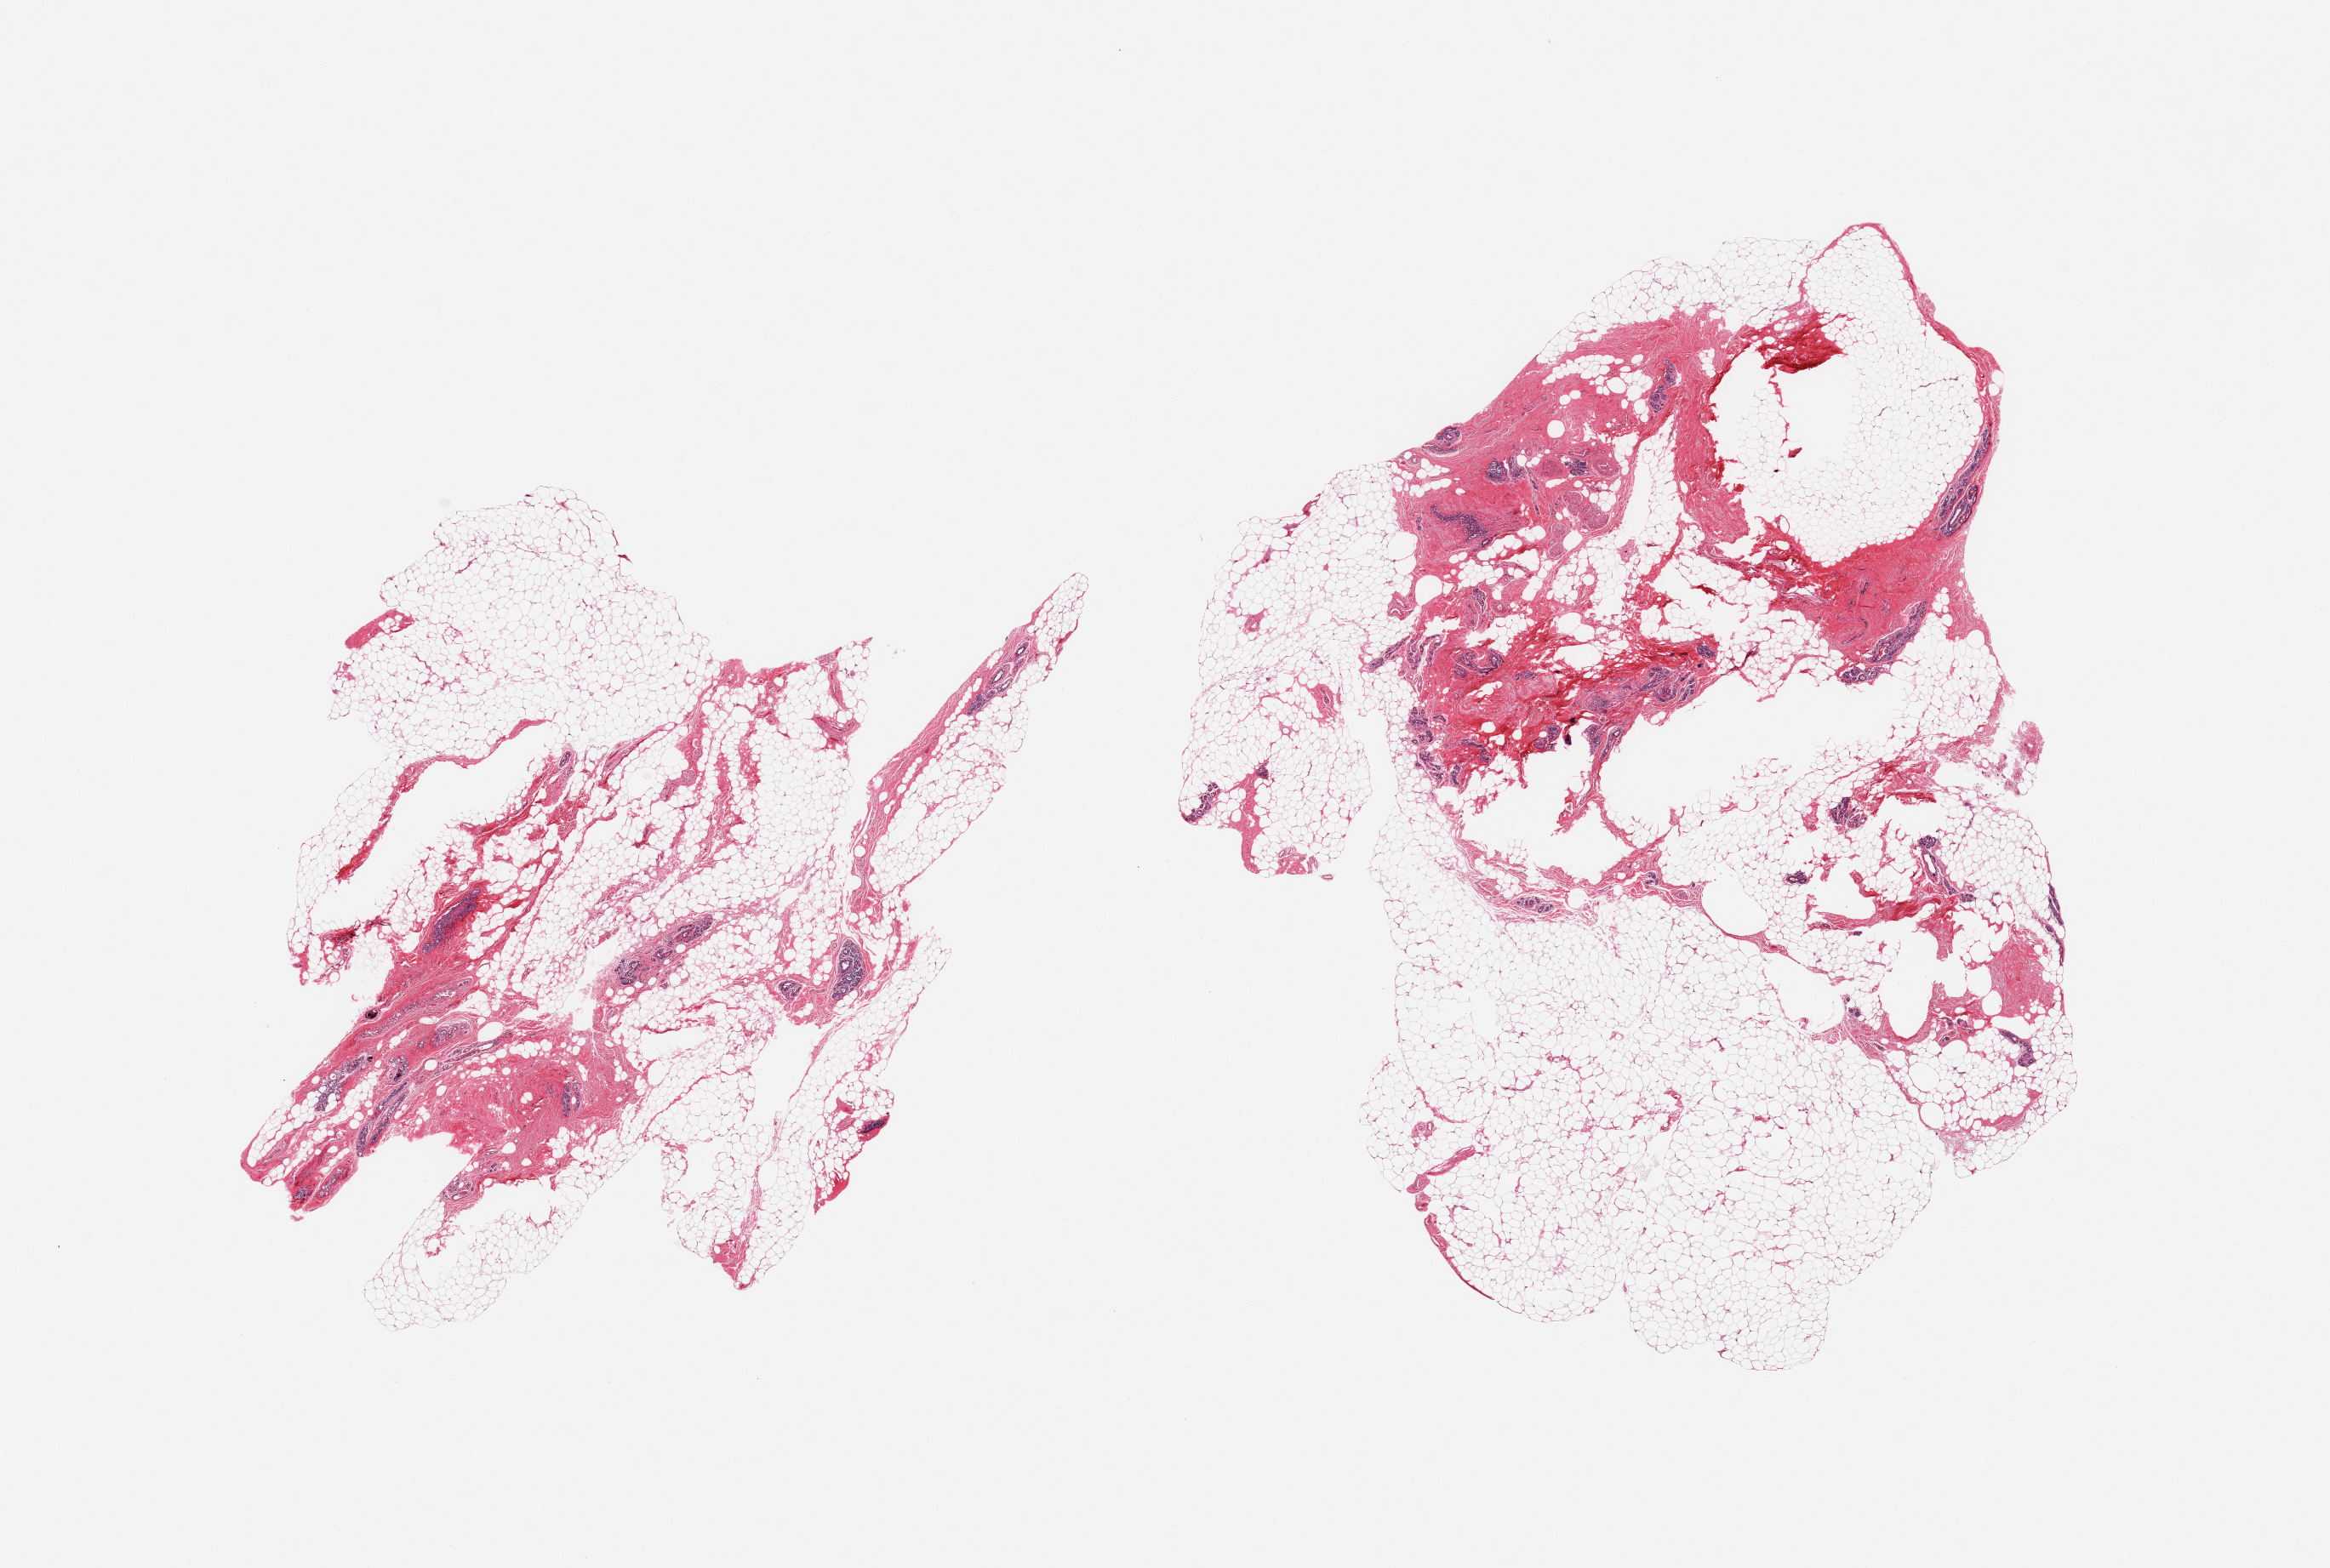
Whole-slide image, haematoxylin and eosin stain, a low-resolution overview of the entire scanned area, about 21.7 x 14.6 mm (from a 20x scan). PAXgene-fixed, paraffin-embedded tissue. Target tissue: breast. Tissue donor sample.
Pathologist's review note for this sample: 2 pieces; scattered ductal & lobular units; 80% fat.